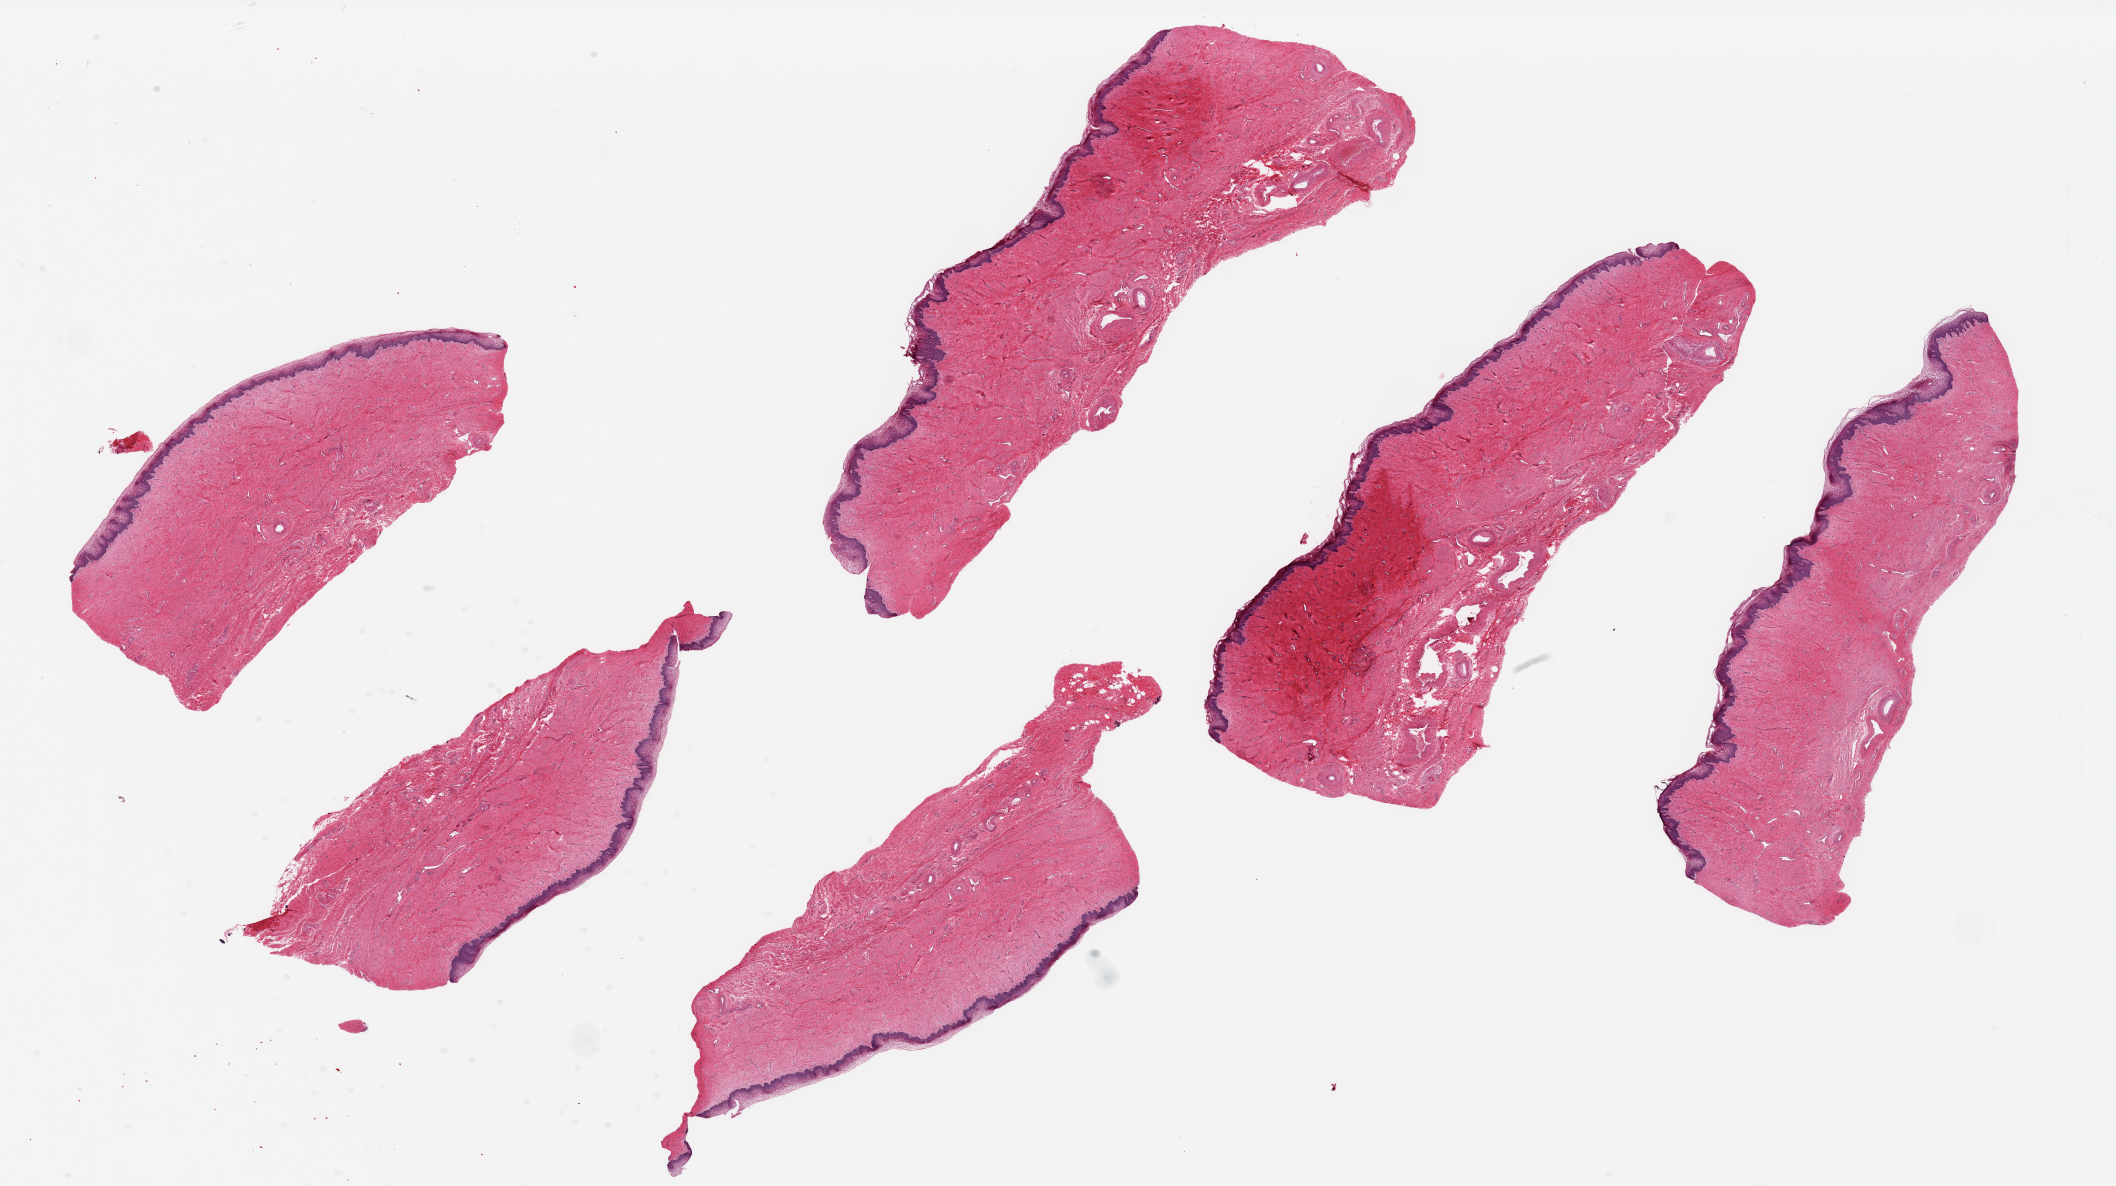
Whole-slide image, H&E stain — shown as a low-resolution overview of the whole scanned area (about 33.5 x 18.8 mm); PAXgene-fixed, paraffin-embedded tissue; sampled site (target tissue): vagina; tissue donor sample. Donor sex: female.
- pathologist's review note for this sample: 6 pieces, up to 11x4 mm